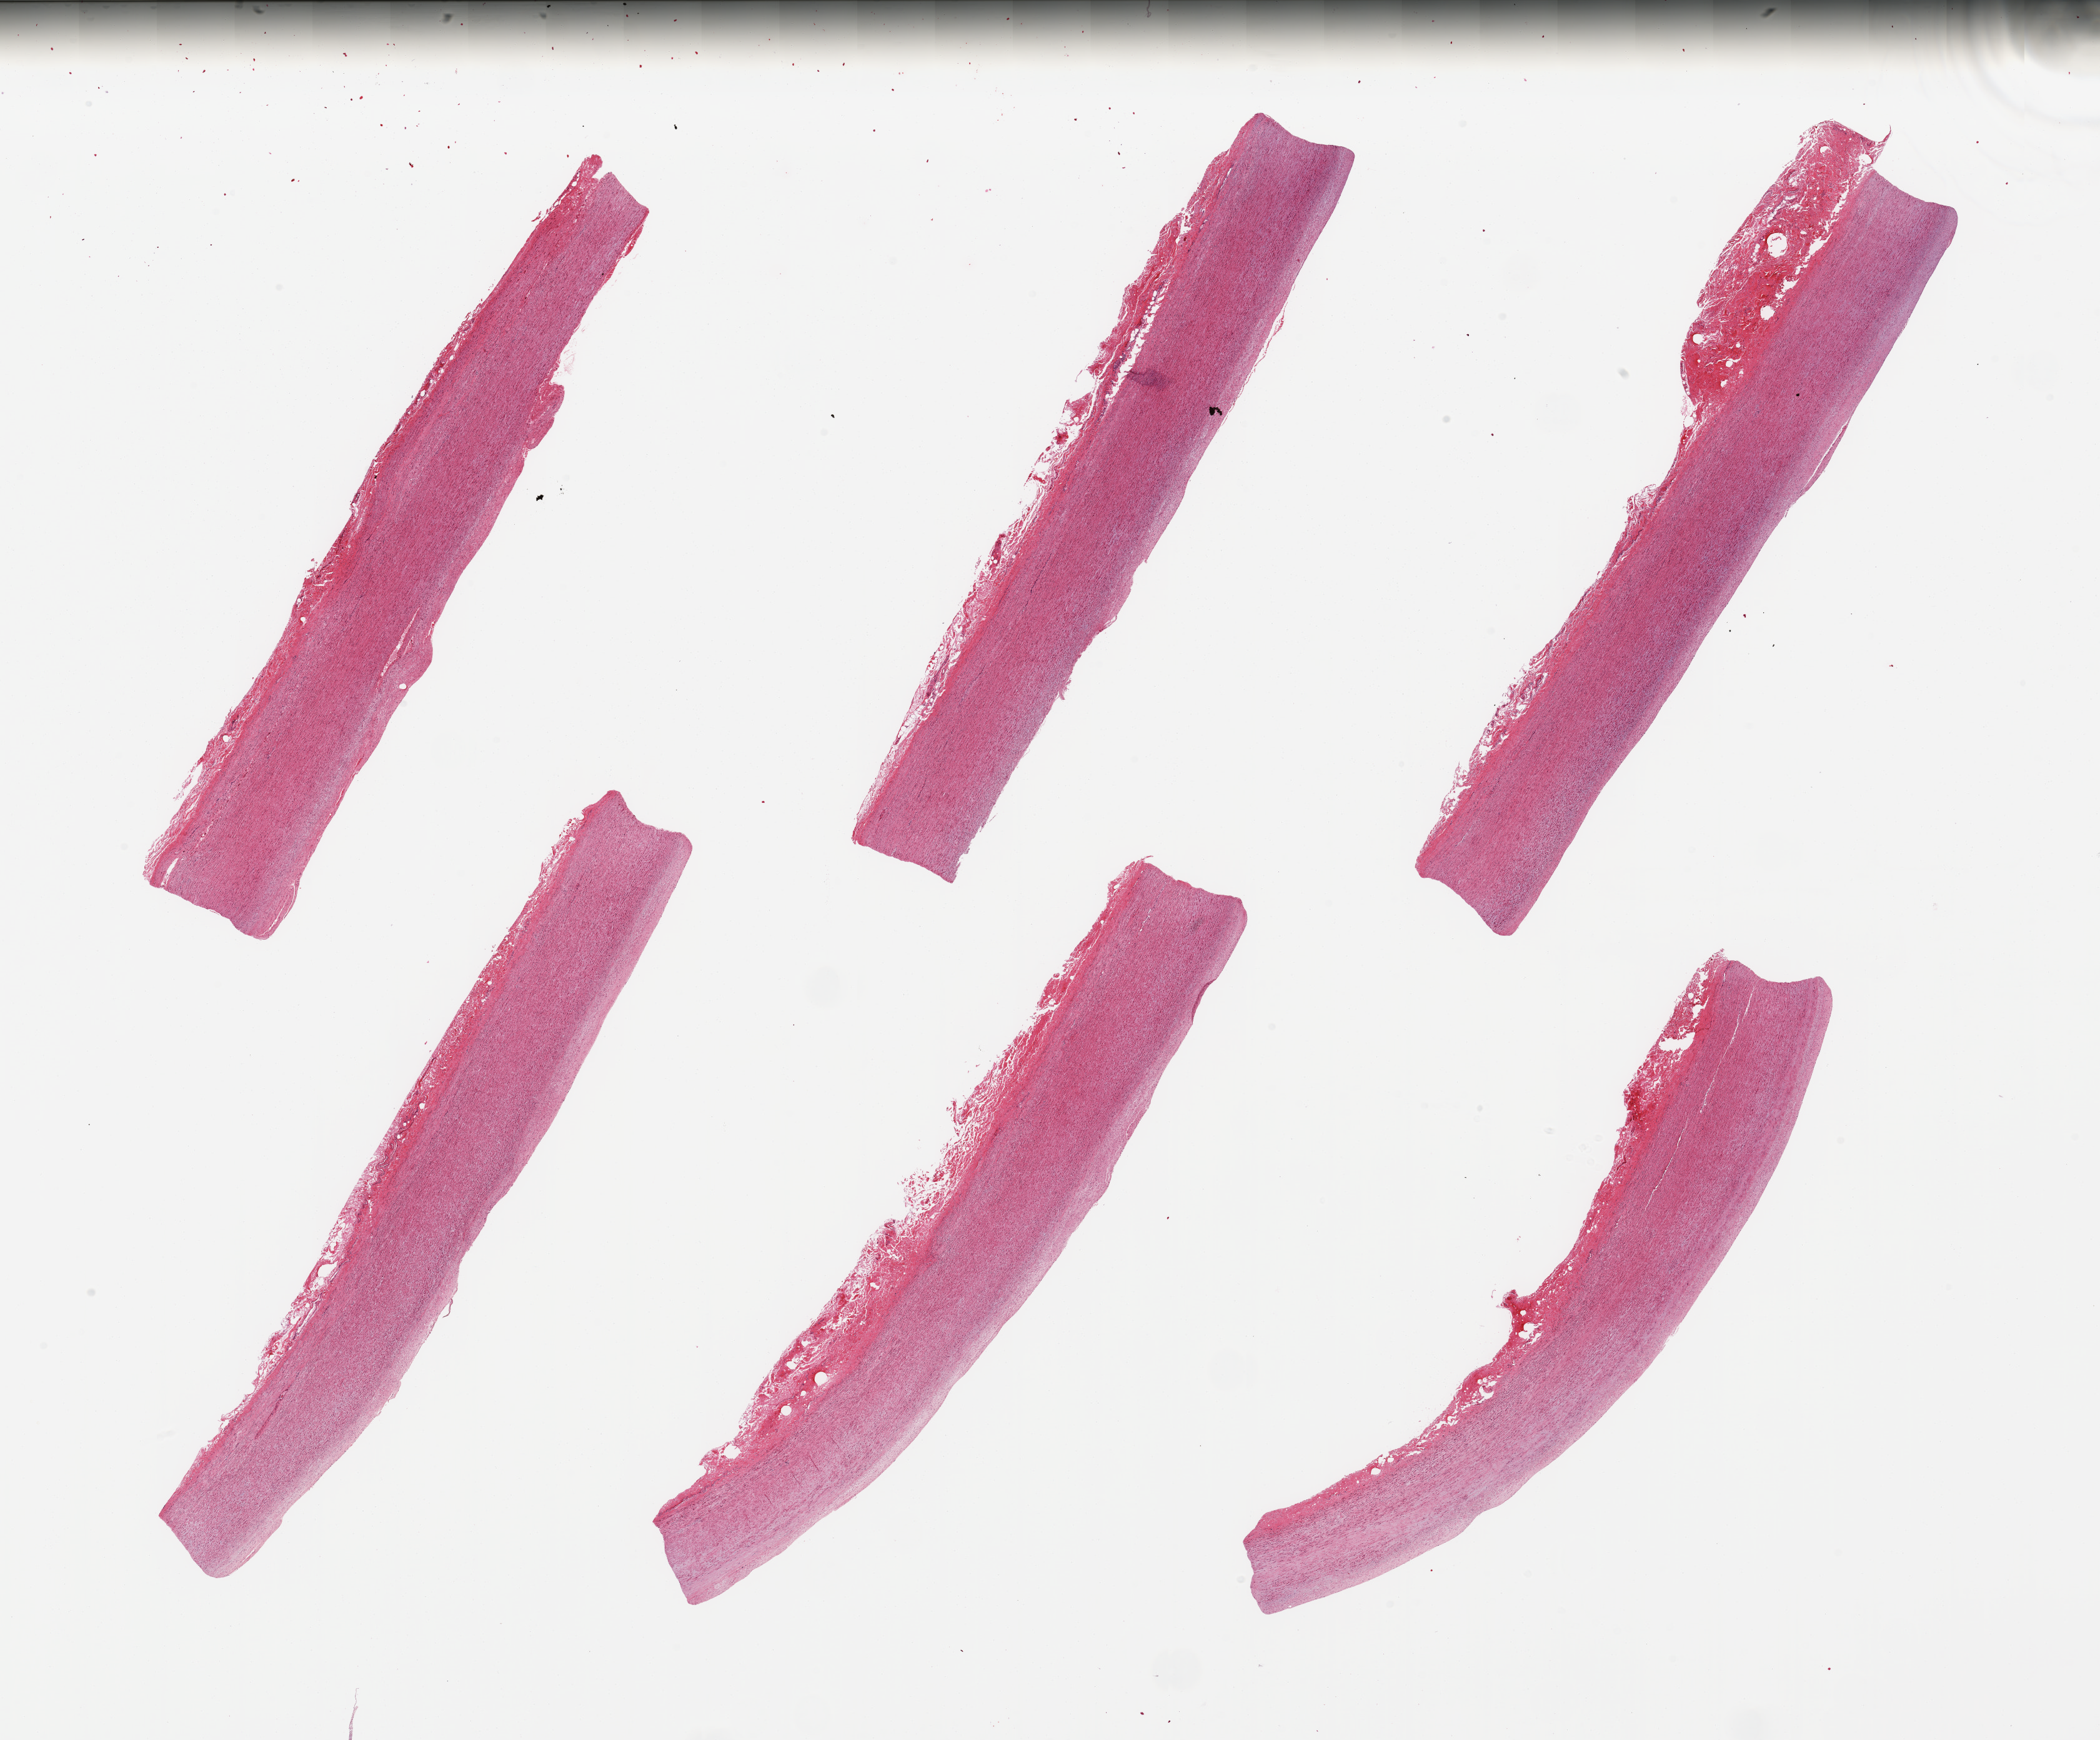
Whole-slide image, hematoxylin and eosin (H&E) stain — whole scanned area (about 26.6 x 22.0 mm) shown as a low-resolution overview; PAXgene-fixed paraffin-embedded (PFPE) section; sampled site (target tissue): aorta; tissue donor sample. Male donor.
Pathologist's review note for this sample: 6 pieces; some plaque.